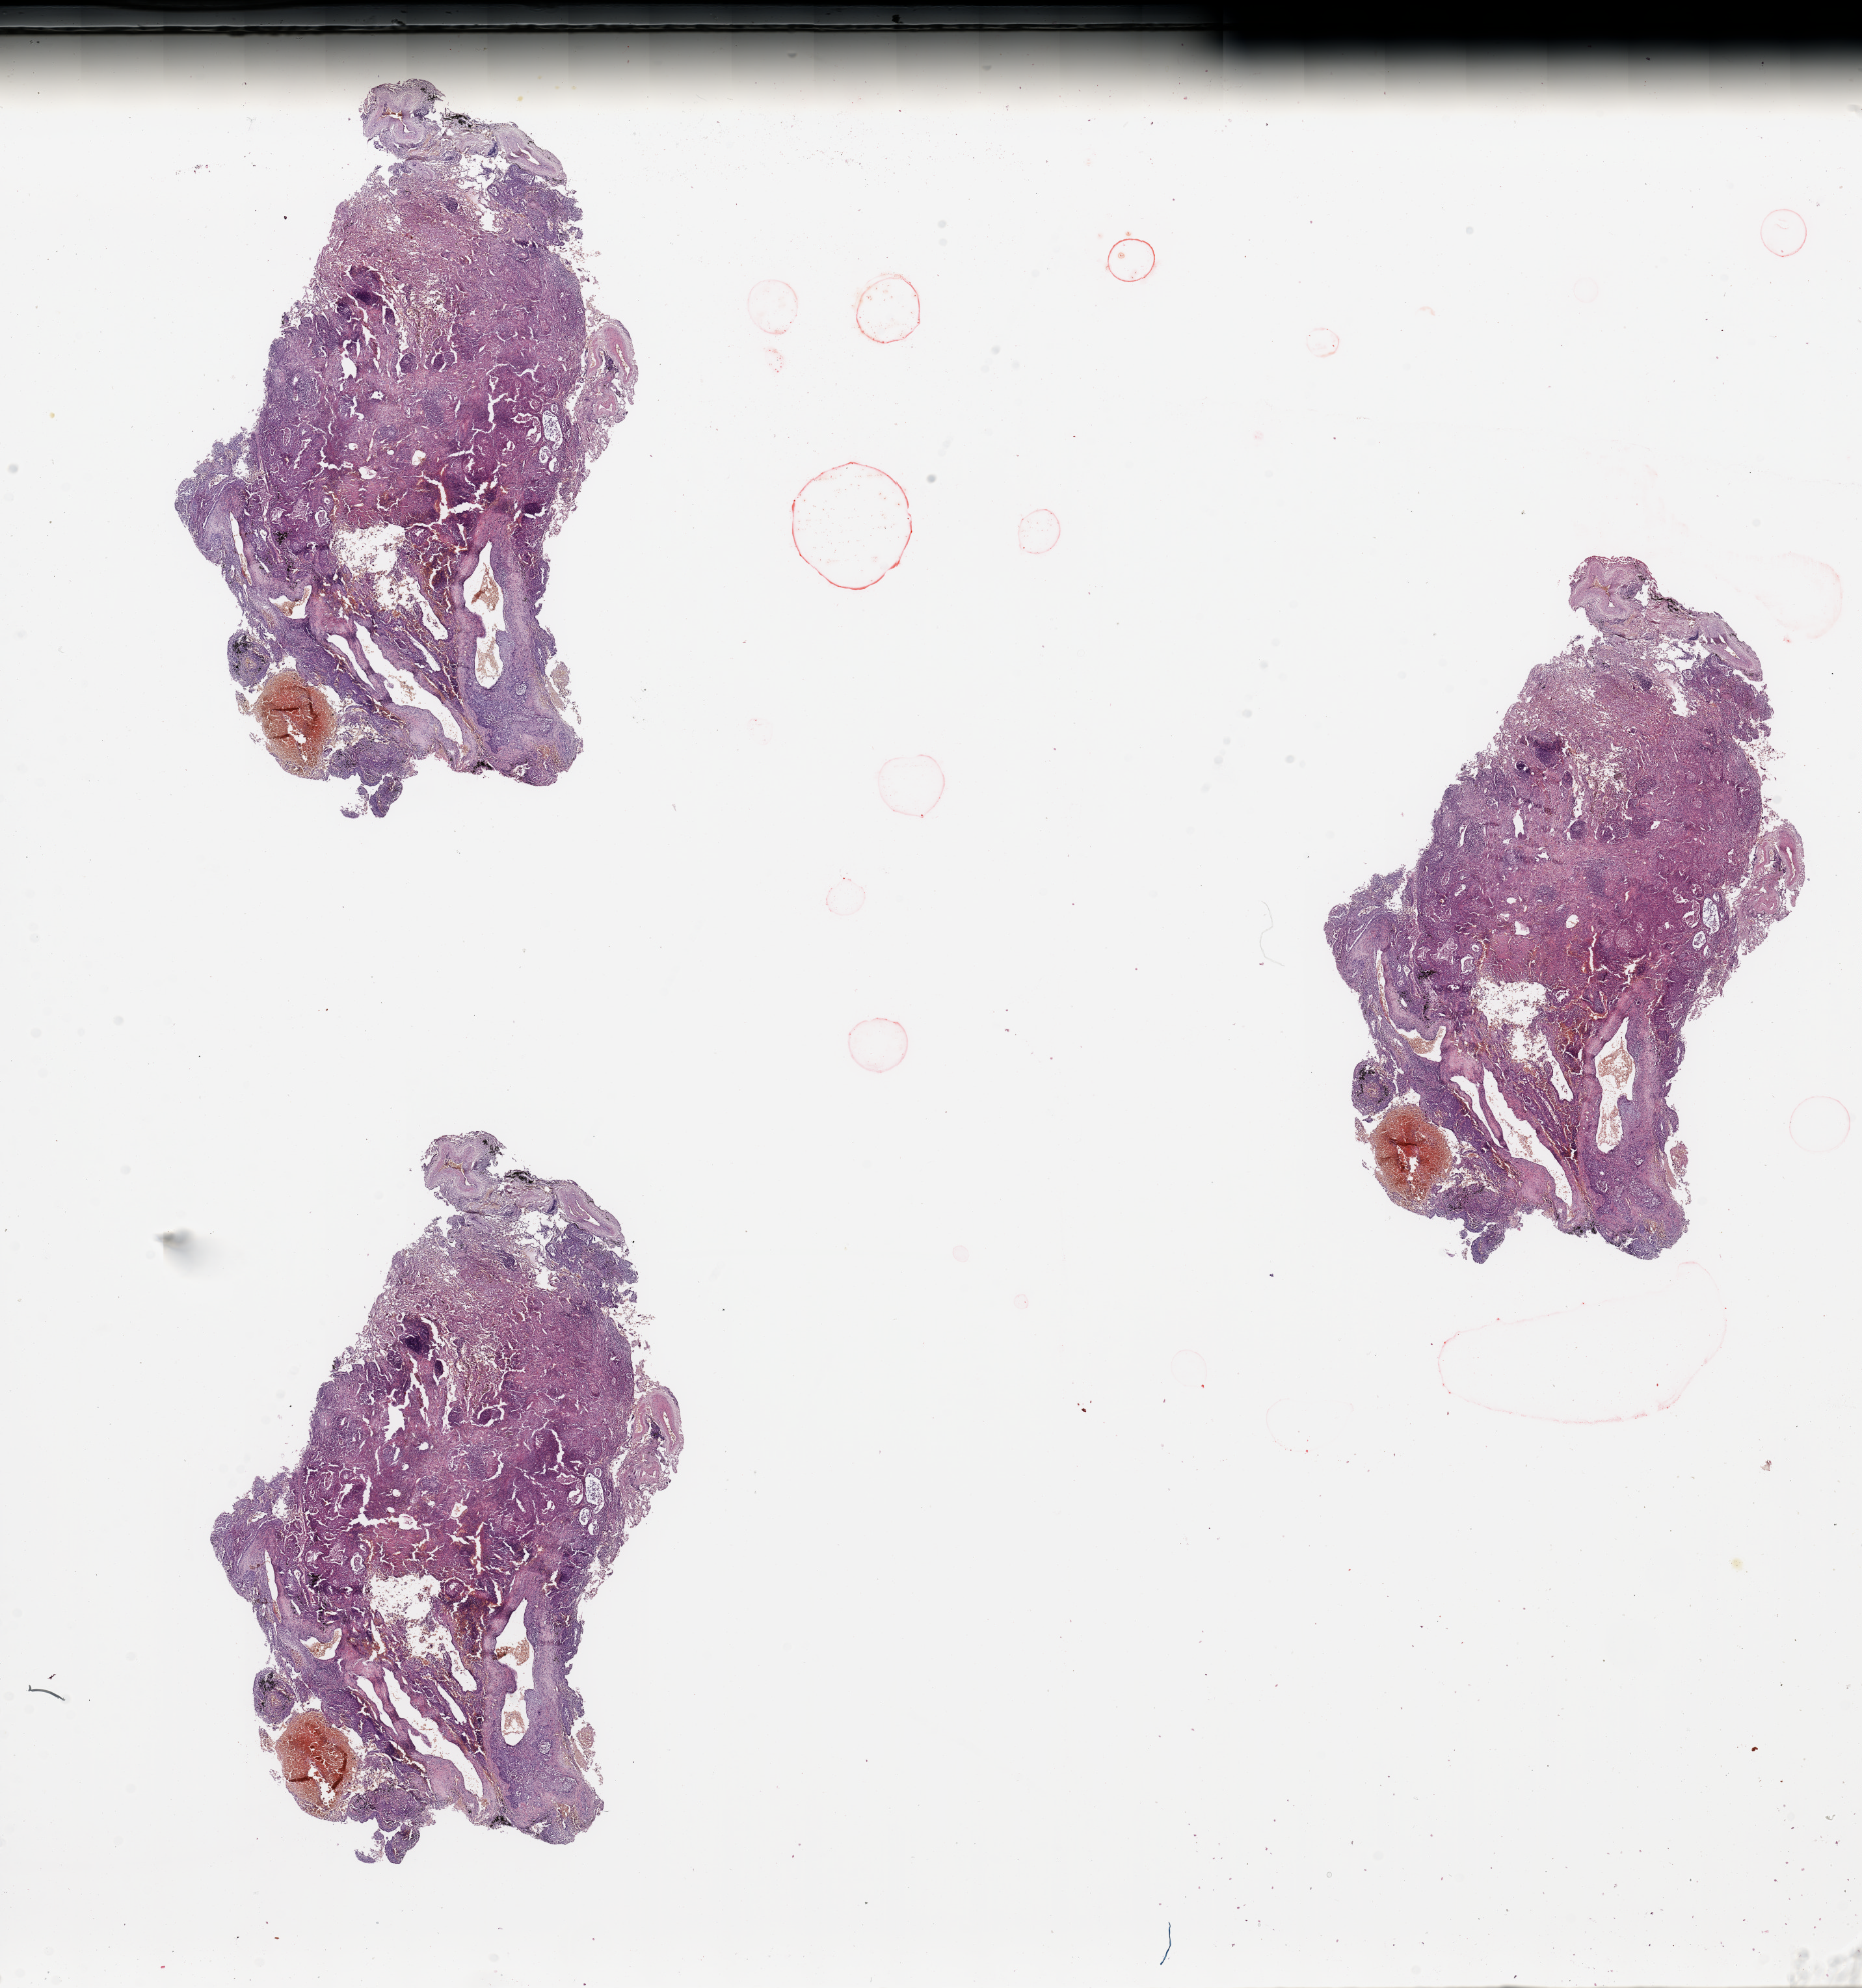
Whole-slide histology image, Hematoxylin and eosin (H&E) stained, whole scanned area (about 22.6 x 24.2 mm) shown as a low-resolution overview, tumour tissue sample, lung. Male, 69 y/o. Histologic grade: GX (grade cannot be assessed).
- histologic diagnosis: Adenocarcinoma, NOS
- AJCC pathologic stage: IA
- primary tumour site (as recorded): left upper lobe